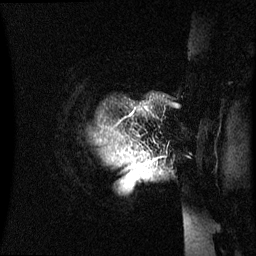
Breast MRI (dynamic contrast-enhanced), one sagittal slice. Position 60 of 60 along the scan axis. Dynamic contrast-enhanced series, image 2 of 3 at this slice position (ordered by acquisition). 1.5 T. TE 4.2 ms, TR 8.4 ms. 256 × 256 image matrix, field of view 230 × 230 mm. Female patient, age 48 years.
Structures marked on this image (semi-automatic segmentation, software-assisted and operator-edited):
- analysis volume of interest (the breast-tissue region the enhancement analysis was run in; not a lesion): bounding box <112,108,186,226> (left, top, right, bottom; pixels)
- tumour enhancement mask (voxels above the 70 % enhancement threshold inside the analysis volume of interest): <136,161,151,167>